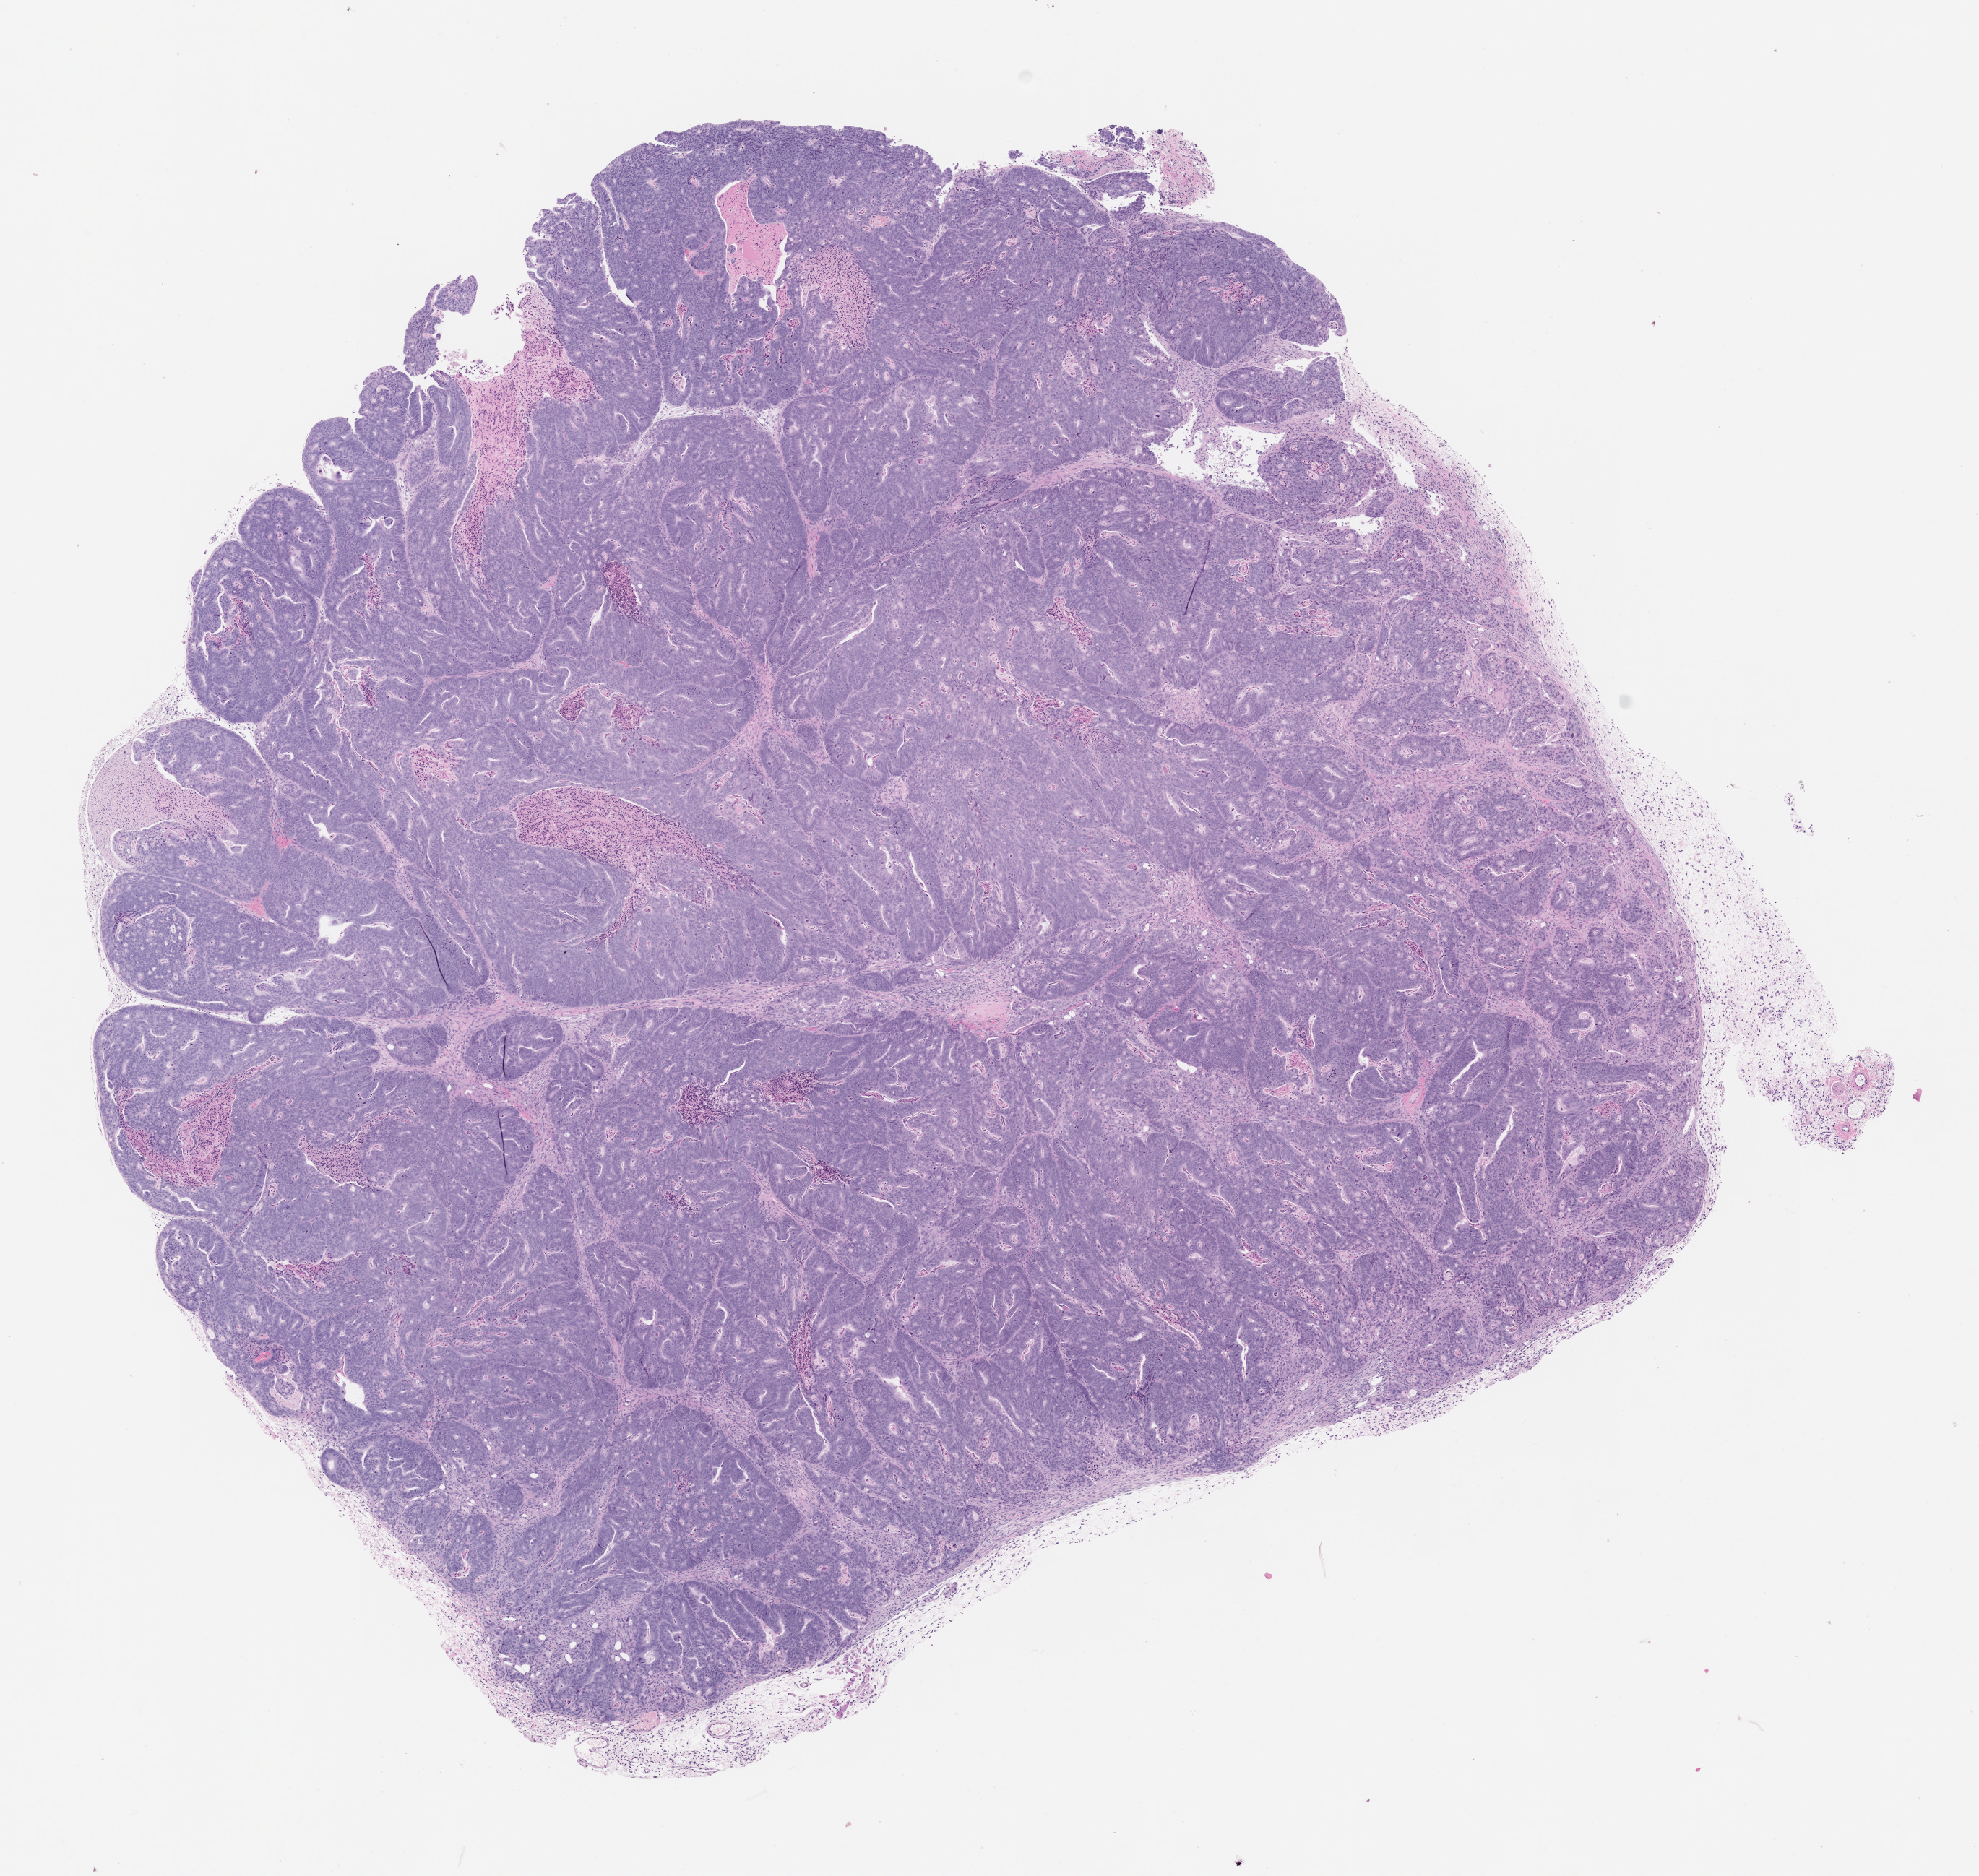
Whole-slide image, H&E: patient-derived xenograft (human tumor grown in a mouse), passage 2, a low-resolution overview of the entire scanned area, about 11.0 x 10.4 mm, FFPE section, tumor site category: colon.
* originating patient diagnosis: Colon Adenocarcinoma